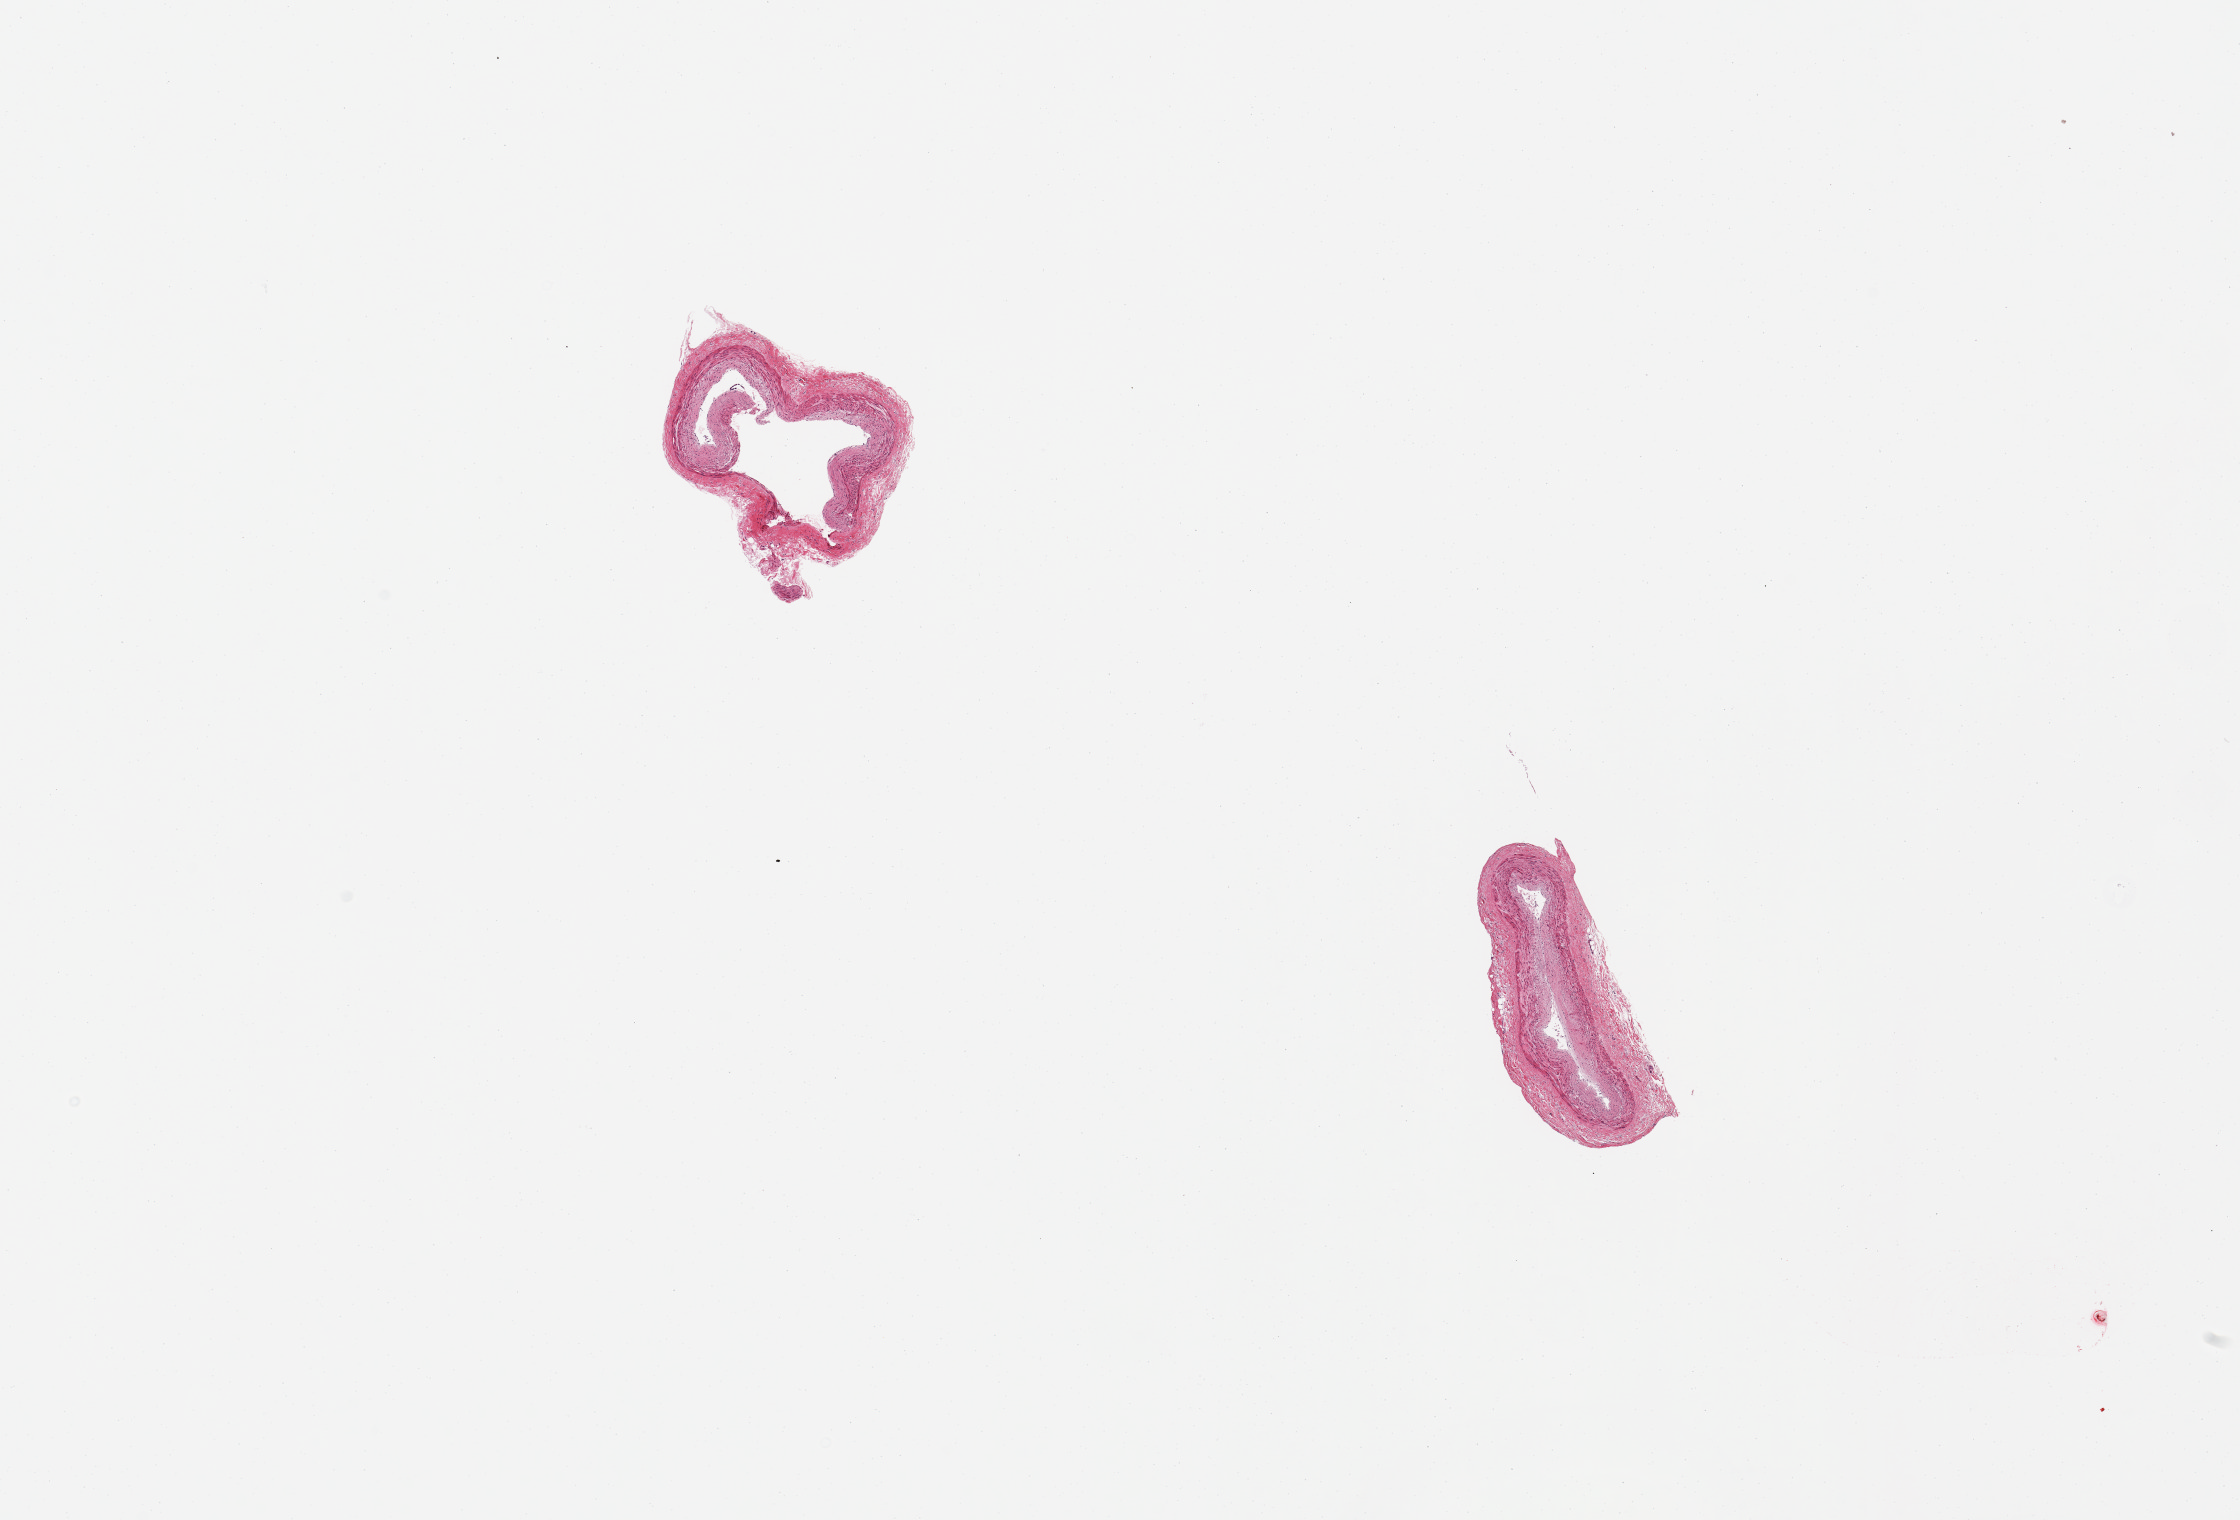
Digitized hematoxylin and eosin (H&E)-stained section, low-resolution overview of the scanned area, about 17.7 x 12.0 mm (from a 20x scan), PAXgene-fixed, paraffin-embedded tissue, target tissue: coronary artery, tissue donor sample. Donor sex: male.
Pathologist's review note for this sample: 2 pieces; slight plaque formation.